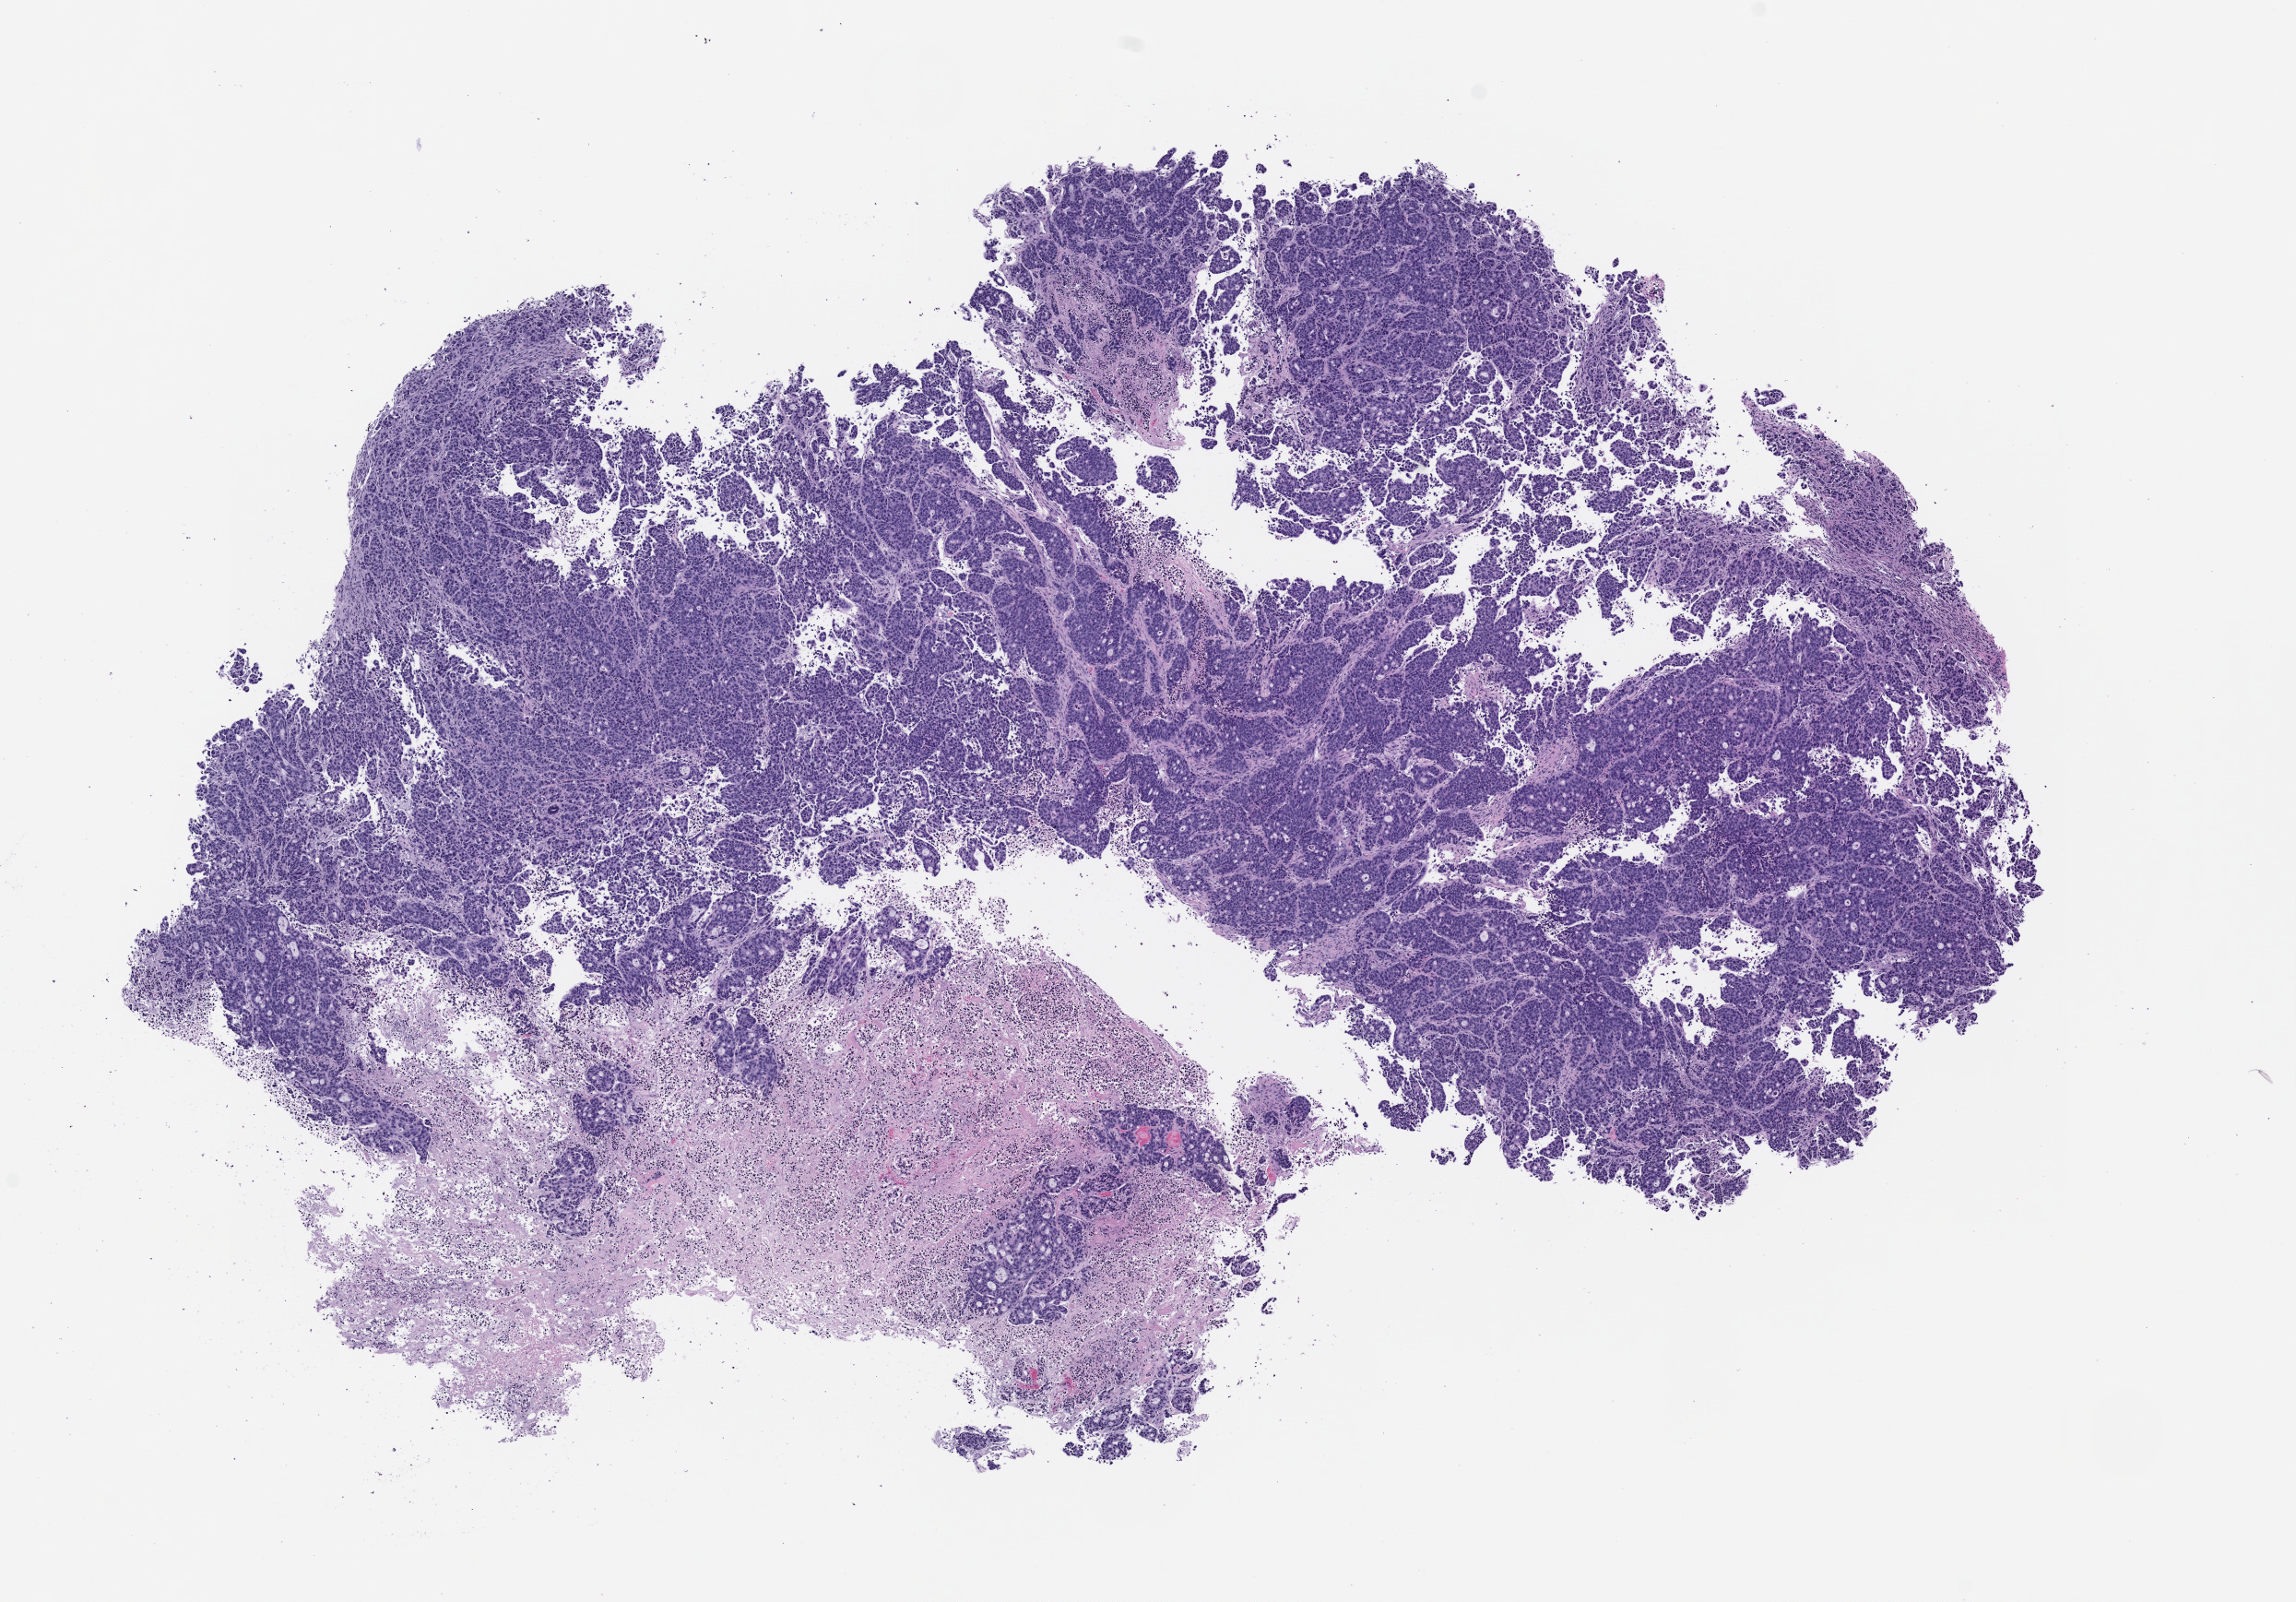
Whole-slide image, hematoxylin and eosin (H&E): patient-derived xenograft (human tumor grown in a mouse), passage 3, whole scanned area (about 10.0 x 7.0 mm) shown as a low-resolution overview; formalin-fixed, paraffin-embedded (FFPE) tissue; tumor site category: colon.
Originating patient diagnosis: Colon Adenocarcinoma.